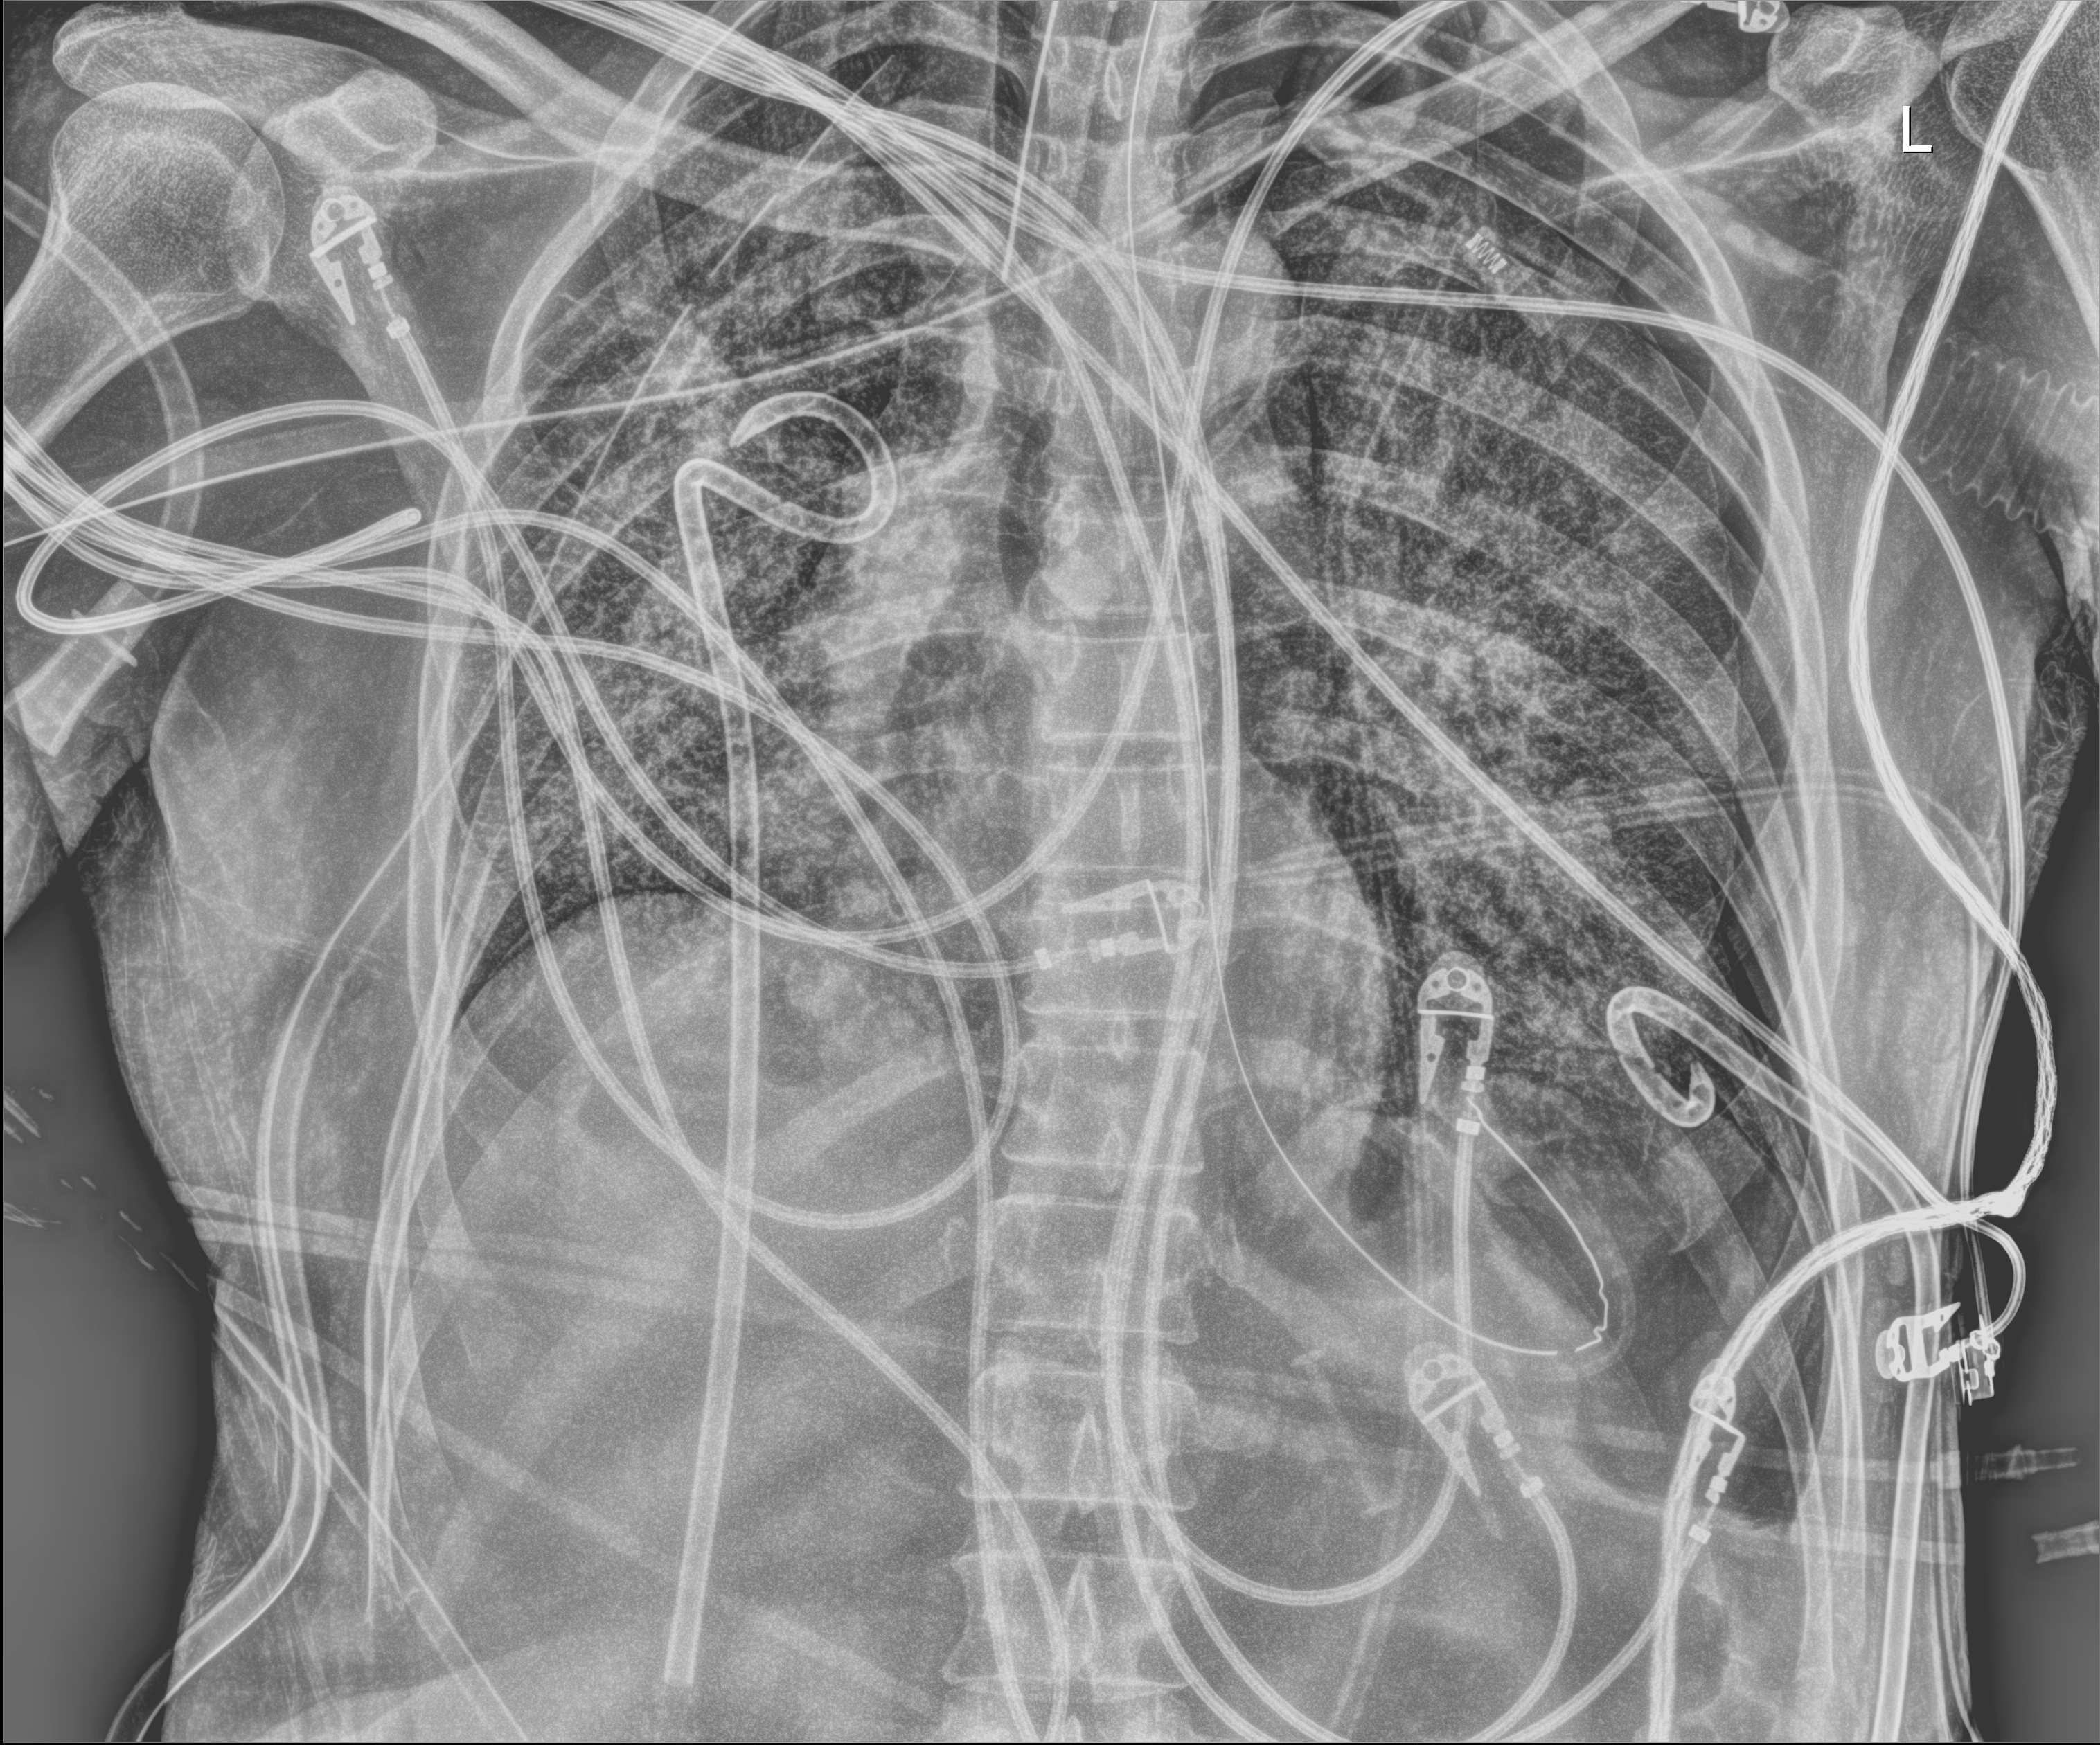
Chest X-ray. Adult patient hospitalised with COVID-19, age 18–59 years.
From the hospital-stay record, not from the radiograph (when in the stay this image was taken is not recorded): admitted to intensive care during this hospital stay: yes; mechanically ventilated during this hospital stay: yes; length of hospital stay: 41 days.